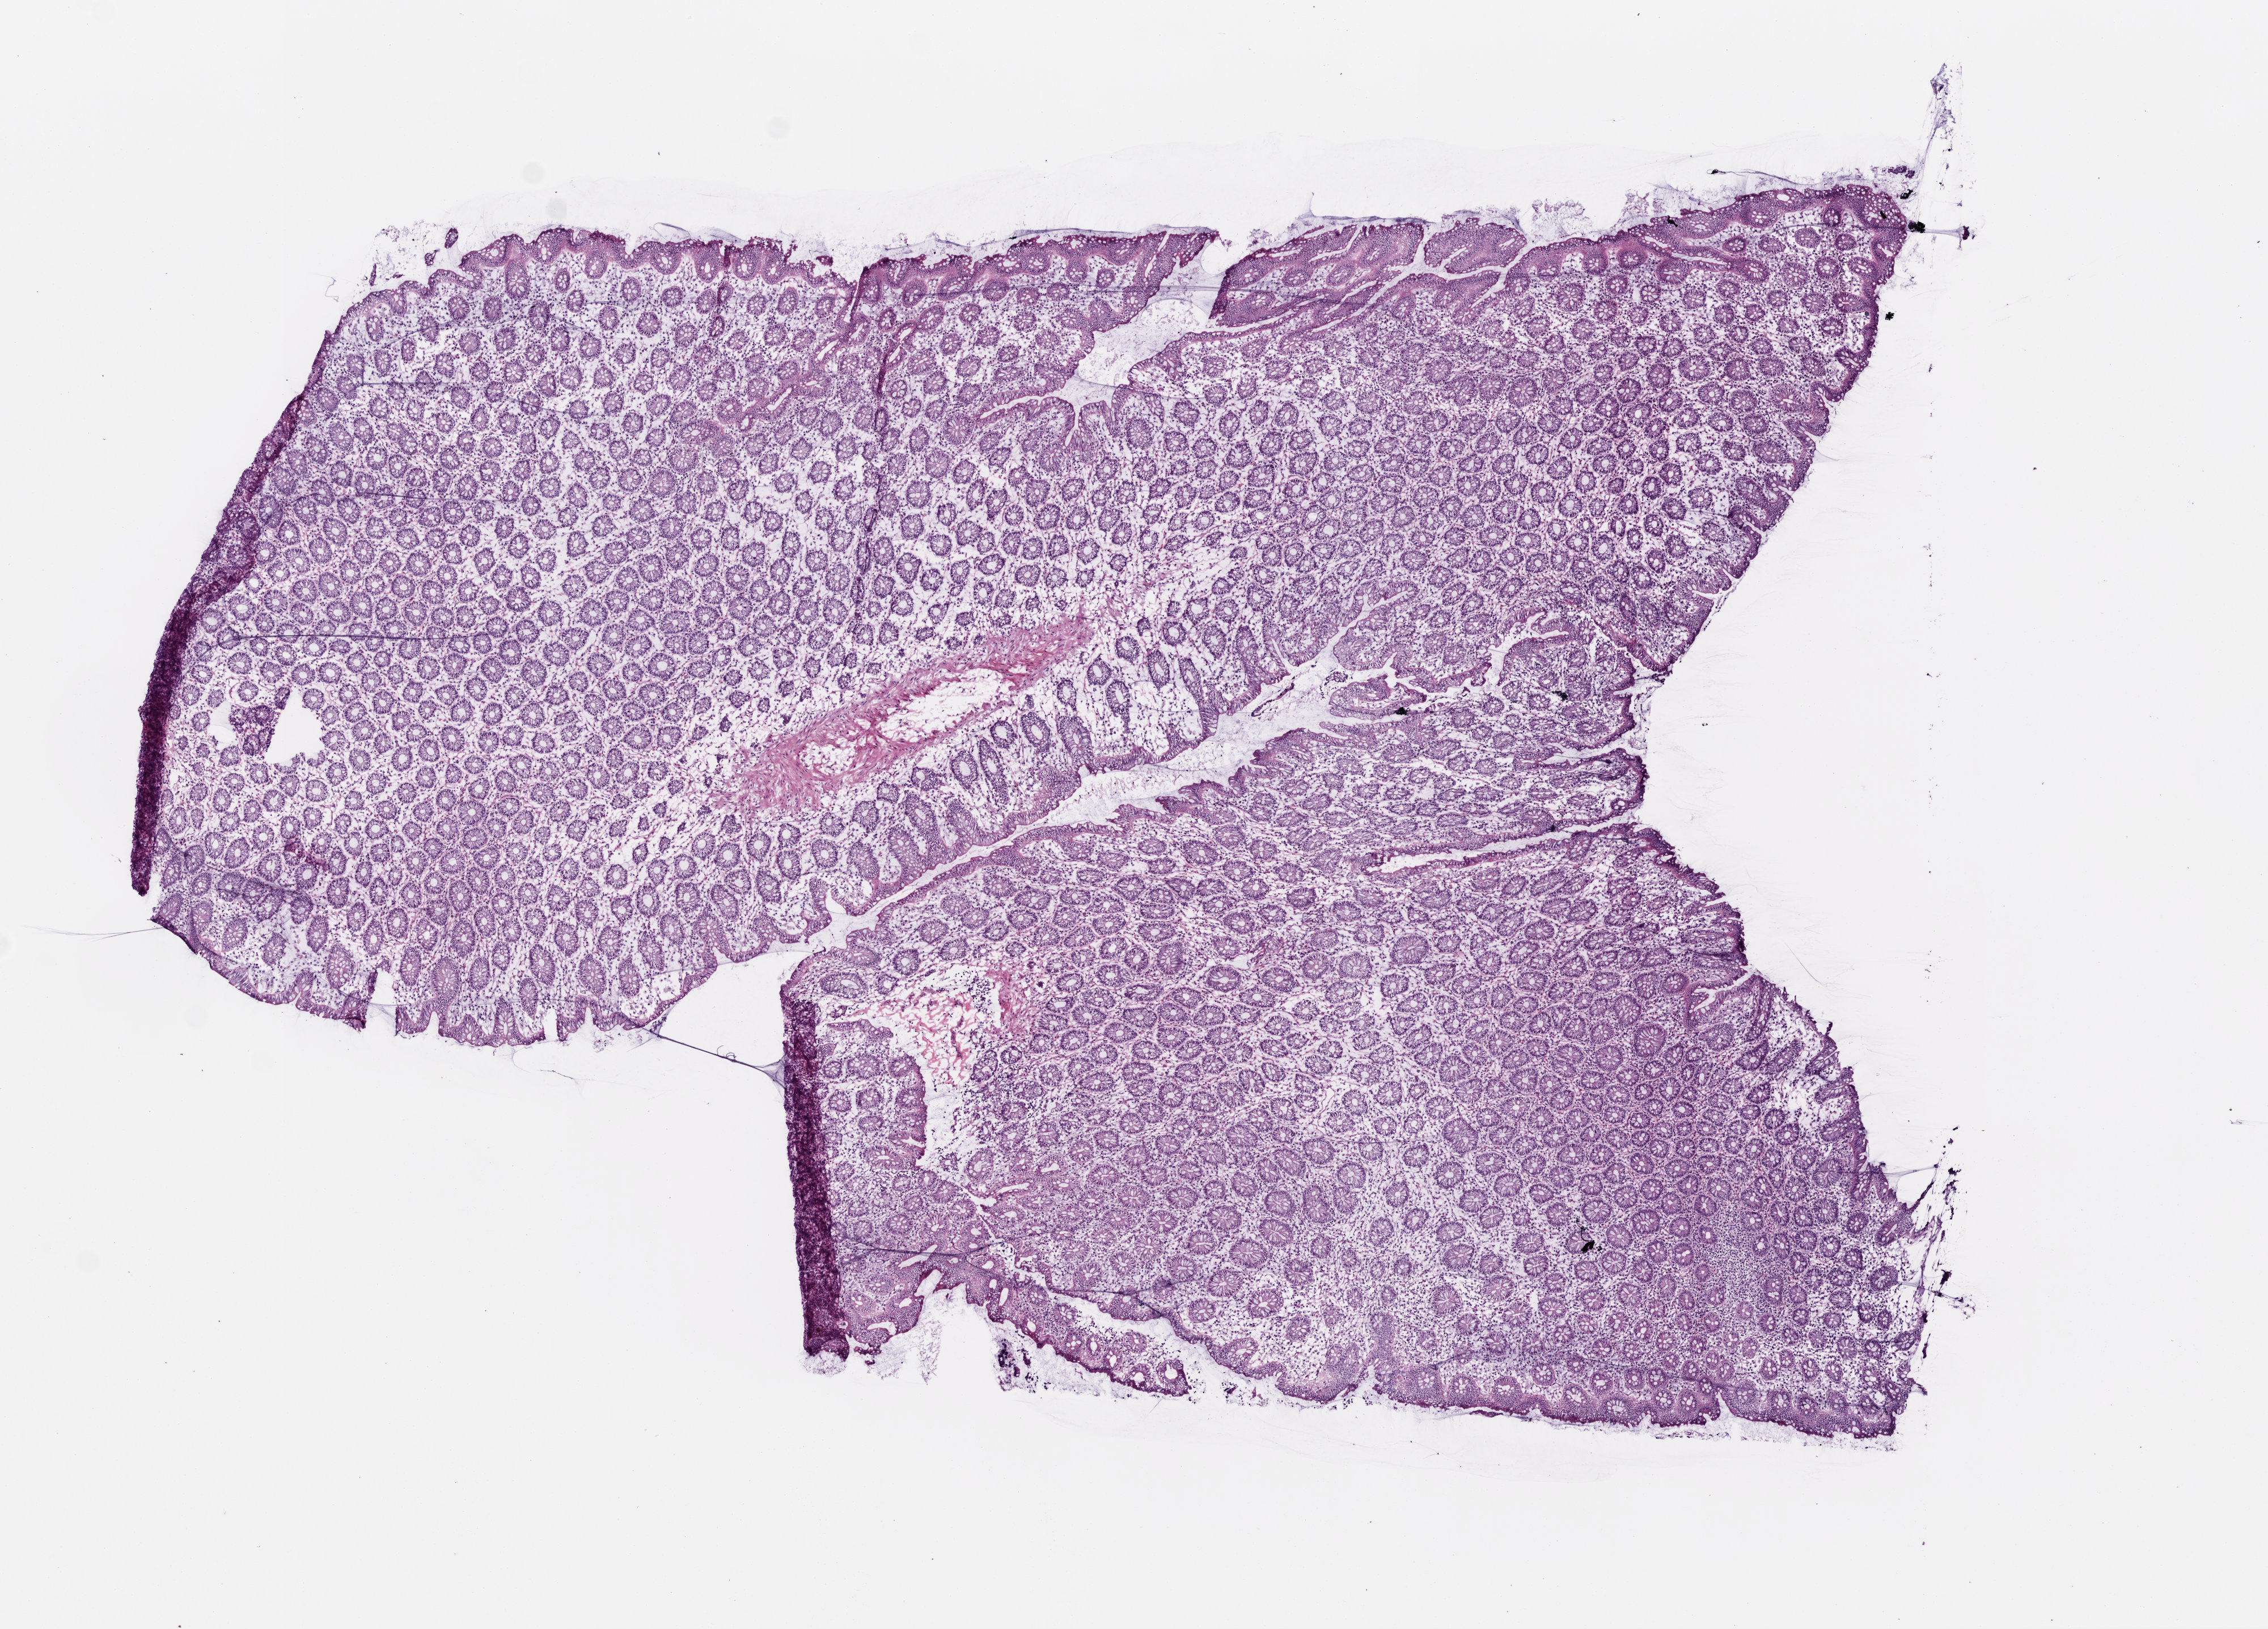
Digitized H&E-stained tissue section (whole slide), a low-resolution overview of the entire scanned area, about 8.0 x 5.8 mm (acquisition: 20x scan), frozen section, colon, solid tissue normal (non-tumour tissue) sample. Female, age 77 years at initial diagnosis.
This section: solid tissue normal (non-tumour) sample from the same patient. Patient diagnosis: Adenocarcinoma, NOS (ascending colon).